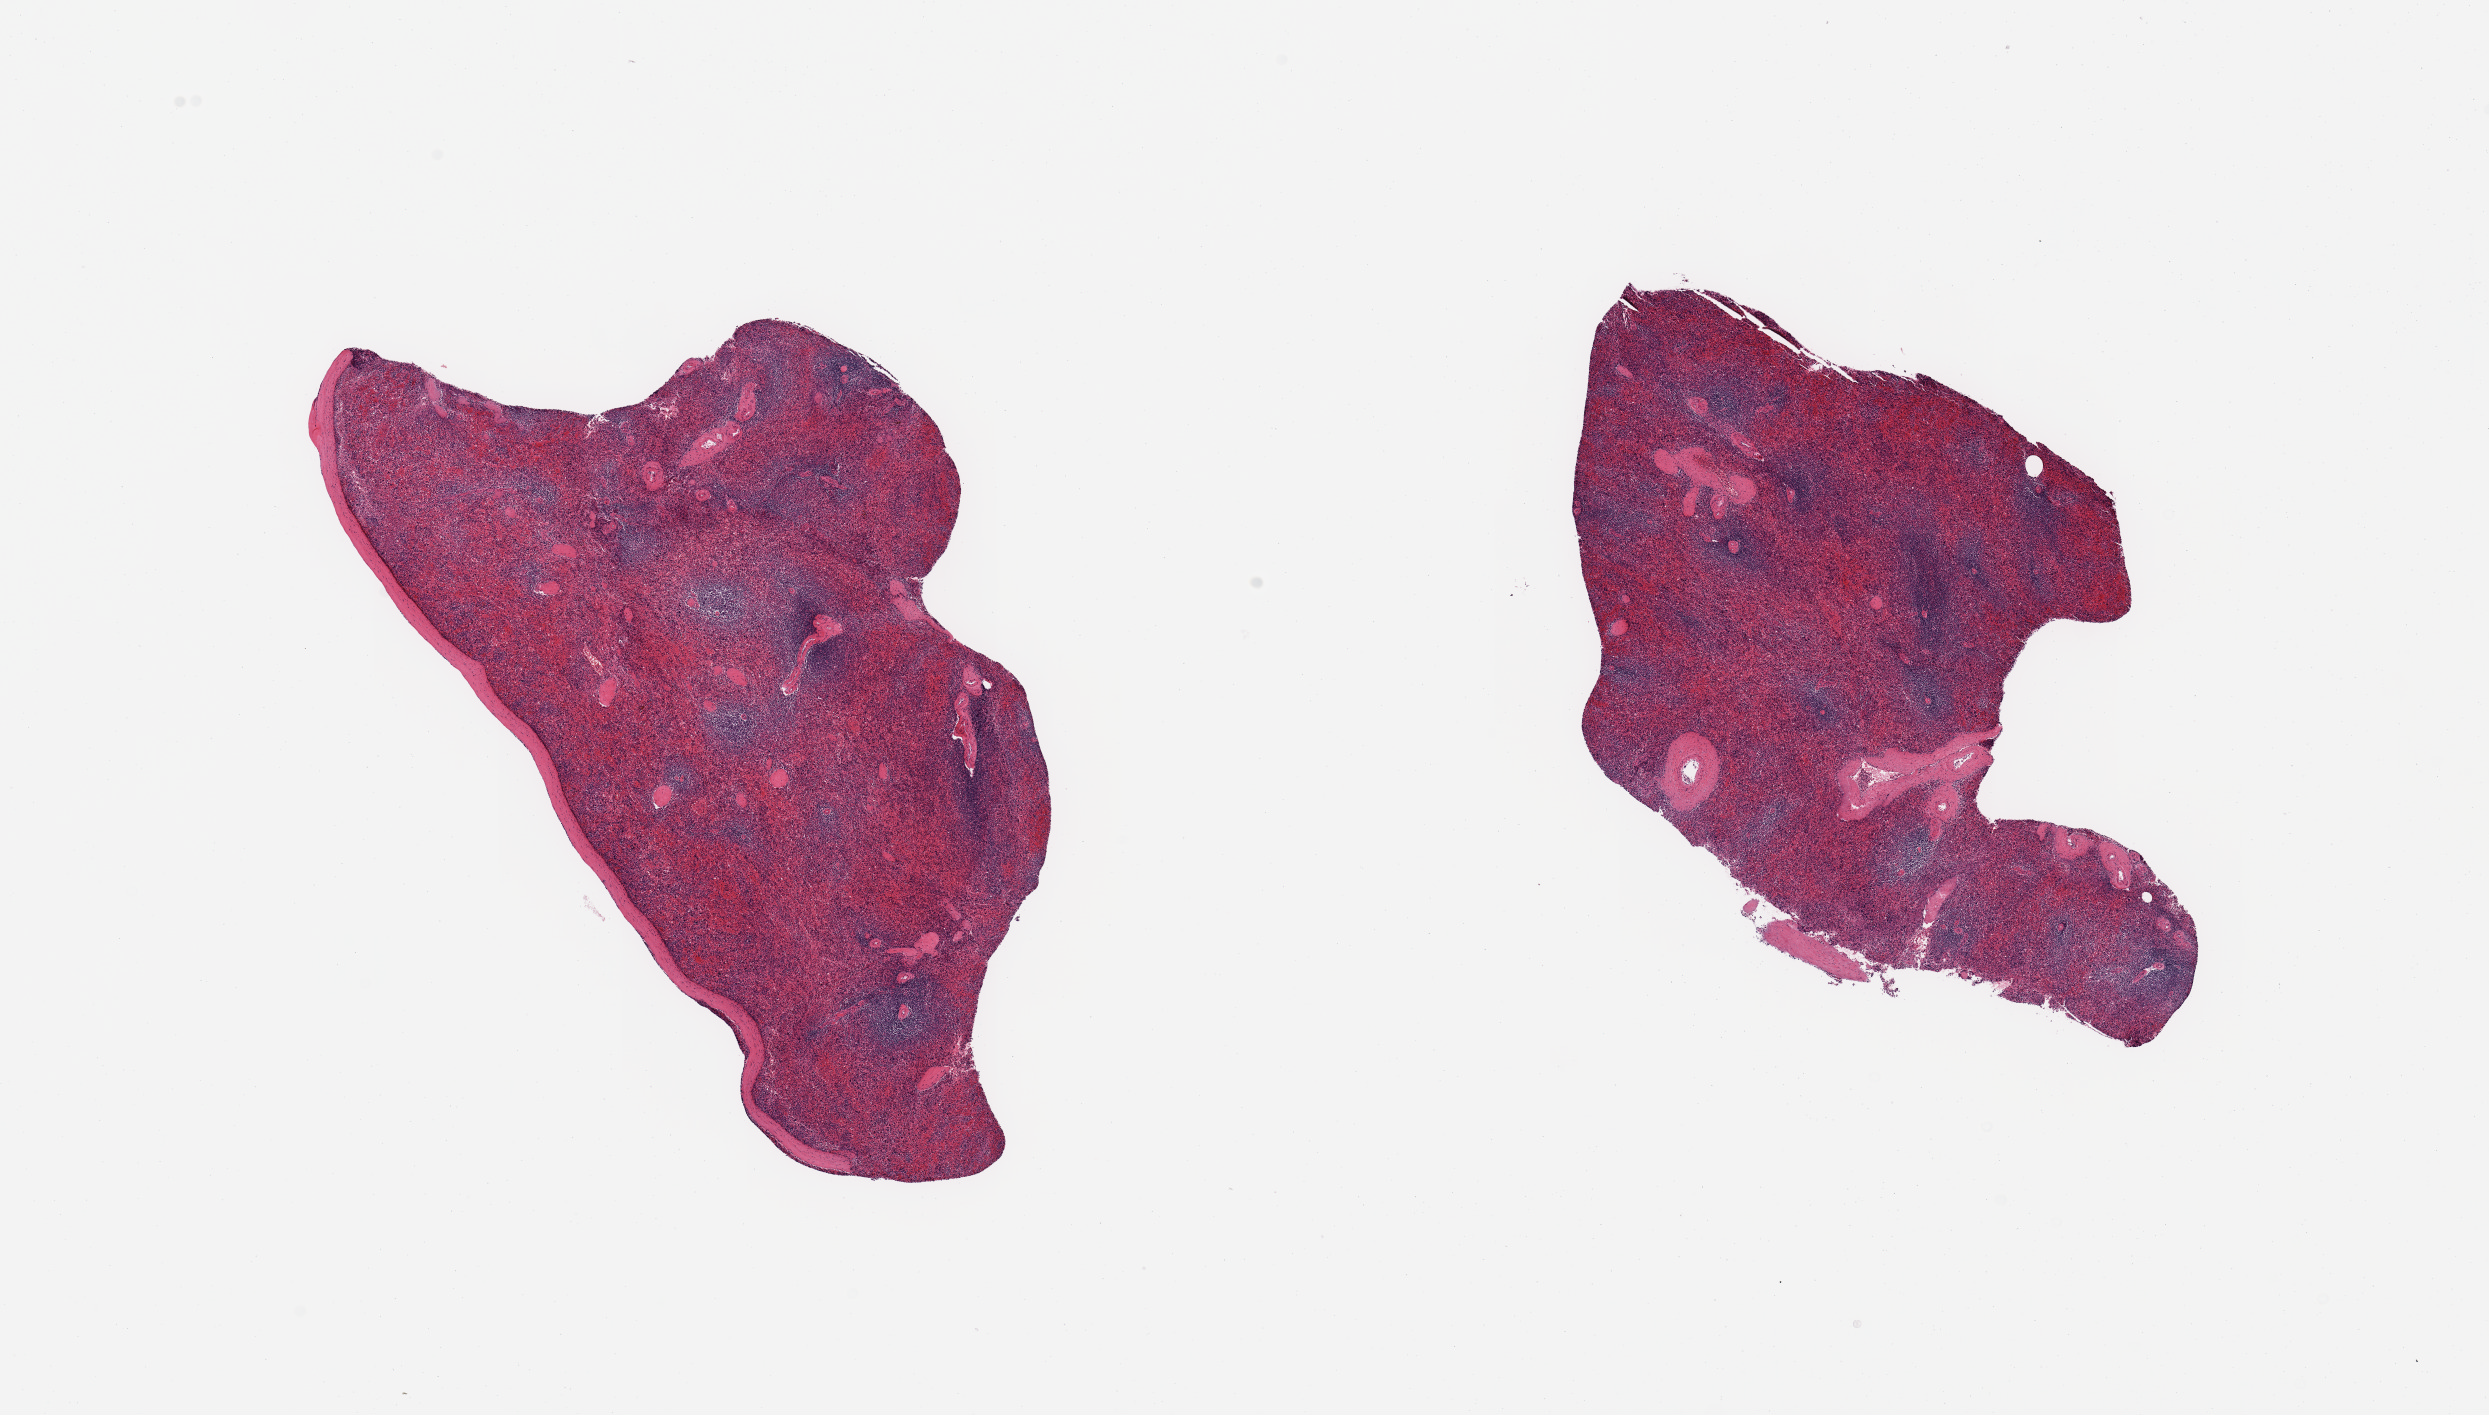
Whole-slide image, haematoxylin and eosin stain, brightfield, whole scanned area (about 19.7 x 11.2 mm) shown as a low-resolution overview, PAXgene-fixed paraffin-embedded (PFPE) section, section of spleen (target tissue), donor tissue sample. Donor sex: male.
Pathologist's review note for this sample: 2 pieces; one piece with outer capsule; congestion.